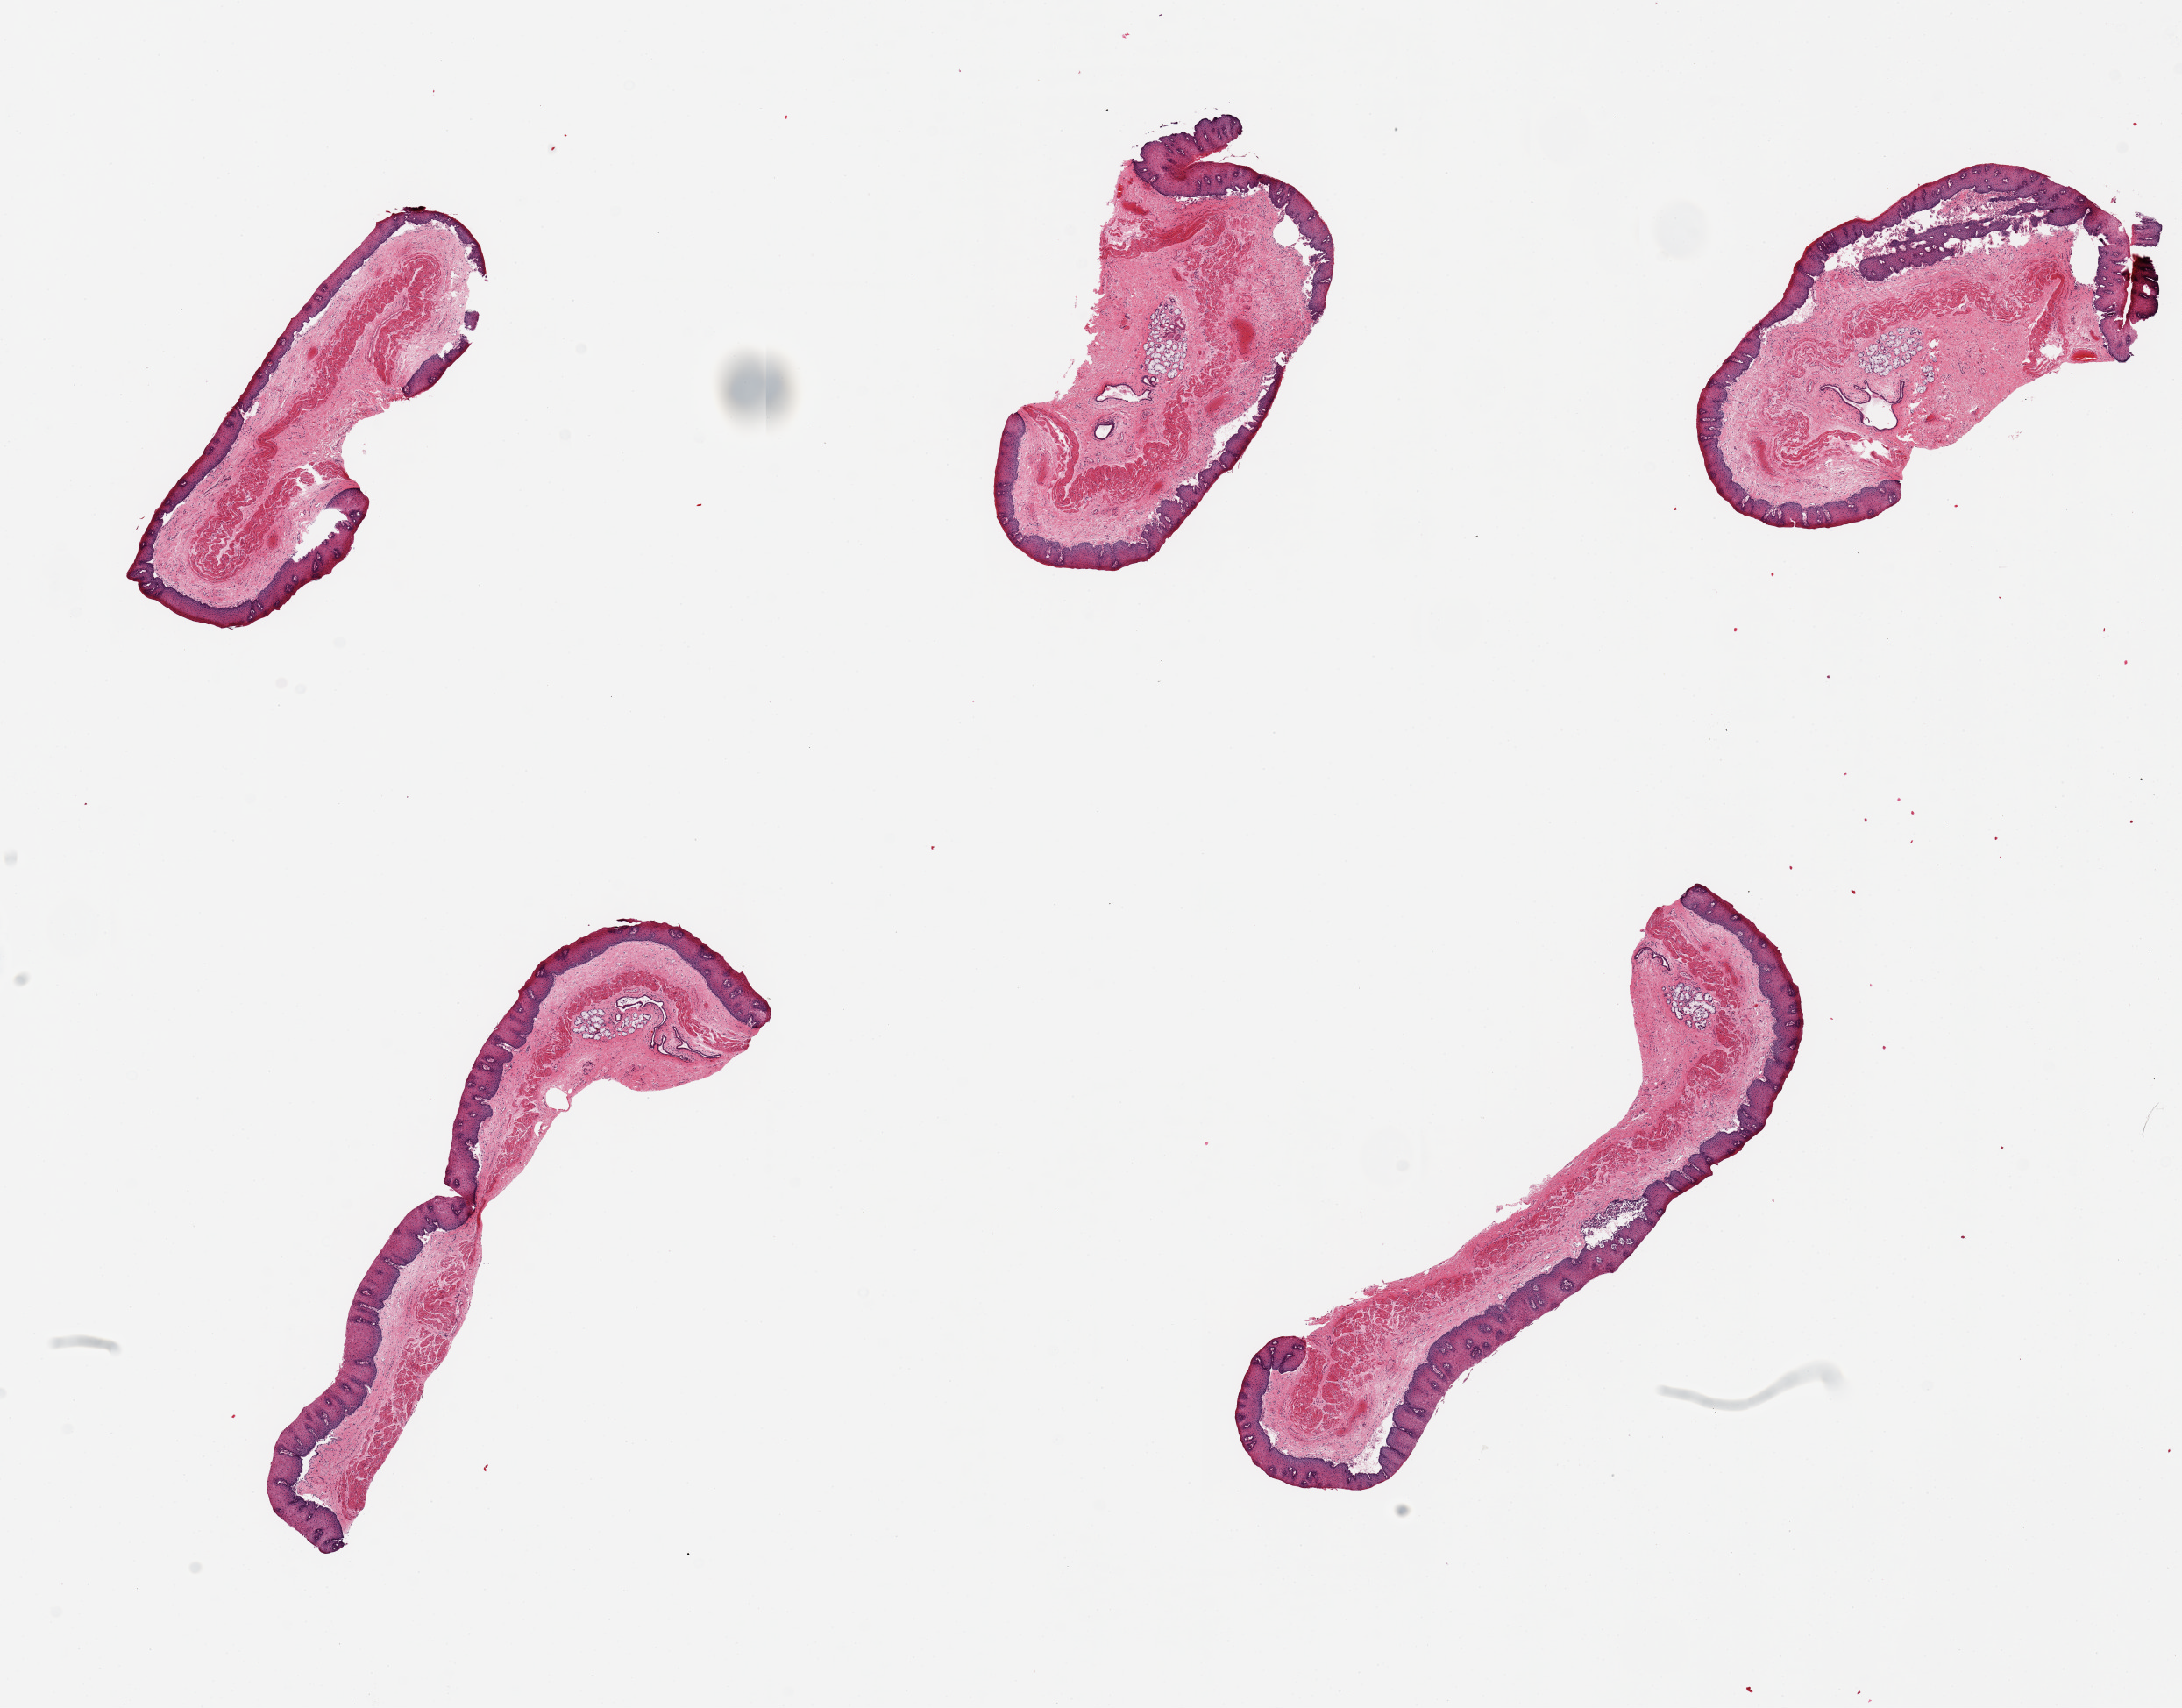
Digitized haematoxylin and eosin-stained section — shown as a low-resolution overview of the whole scanned area (about 19.7 x 15.4 mm, slide scanned at 20x). PAXgene-fixed paraffin-embedded (PFPE) section. Sampled site (target tissue): esophageal mucous membrane. Tissue donor sample. Donor: male.
- reviewer comment on this tissue sample: 6 pieces, squamous mucosa beginning to slough, a few submucosal glands noted